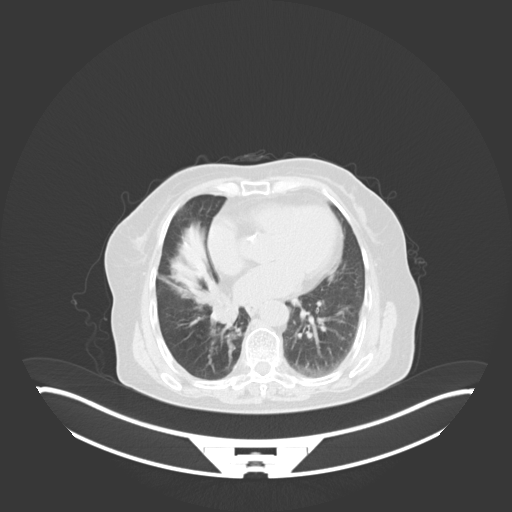
Chest CT, one axial slice; slice 20 of 76 in the series (ordered by position); lung window (W 1500 / L -600 HU); 3 mm slice thickness; 512 × 512 image matrix, field of view 500 × 500 mm. Patient: female, 75 years. Case-level facts recorded for this patient, not image findings: clinical TNM (as recorded): T1b N0 M1a.
Annotated regions visible in this slice (bounding box drawn by a radiologist):
- lung tumour (recorded histology: squamous cell carcinoma): box from (x=205, y=296) to (x=238, y=324) px